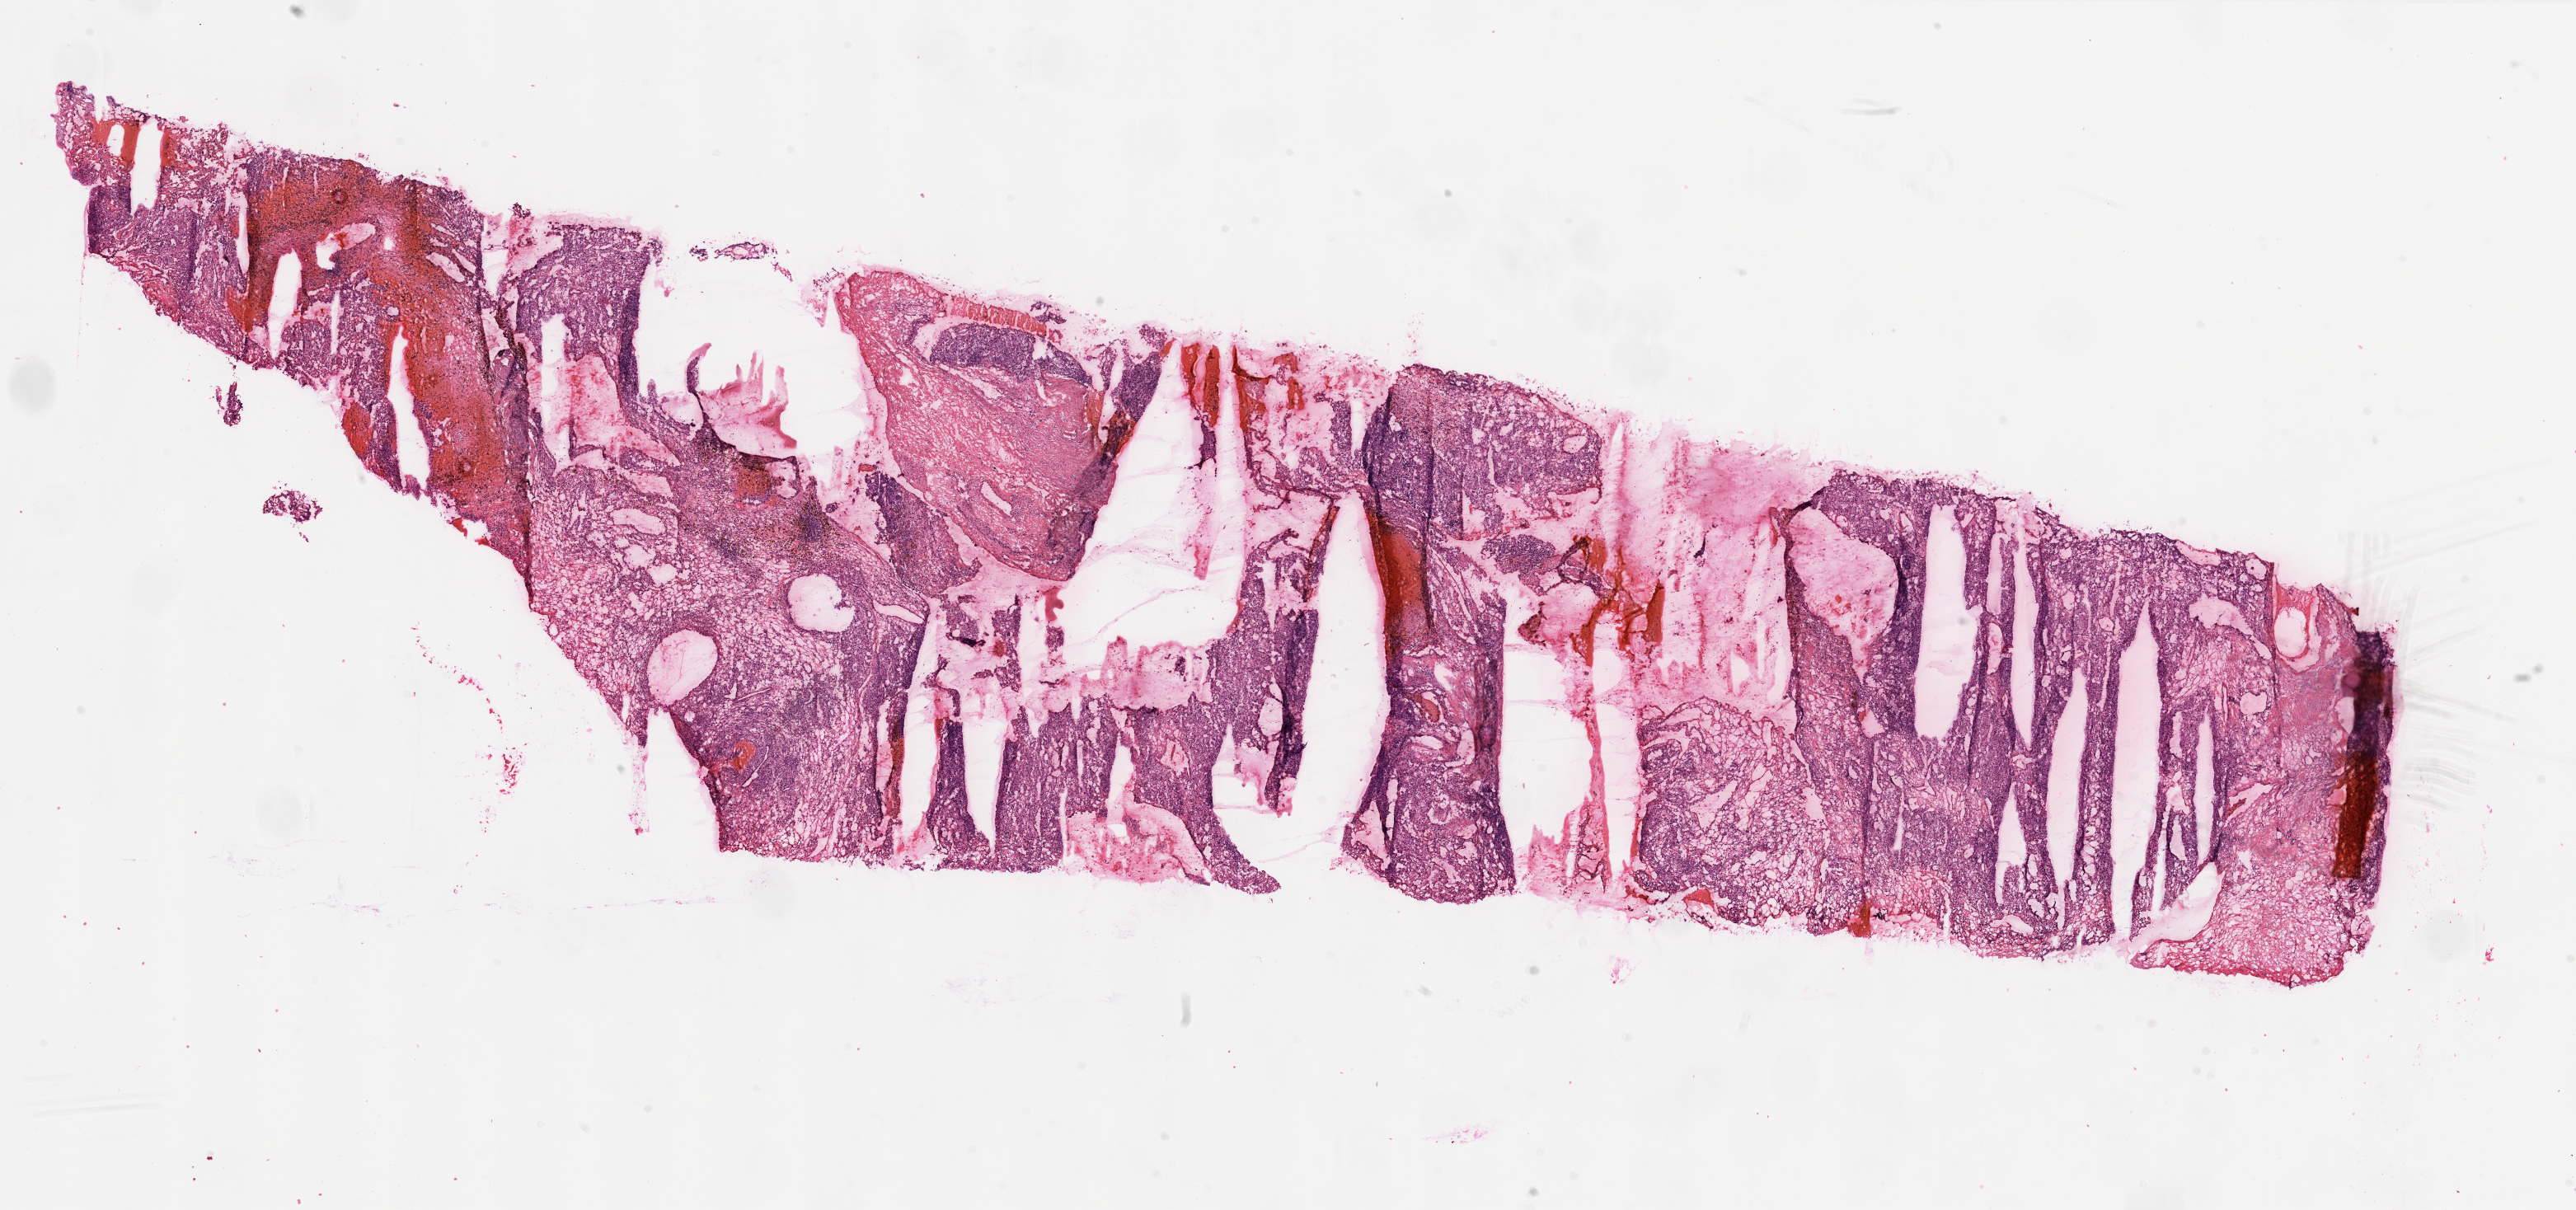
Digitized Hematoxylin and eosin (H&E) stained tissue section (whole slide), low-resolution overview of the scanned area, about 25.1 x 11.8 mm. Frozen section from the top of the tissue portion. Sample: primary tumour, kidney. Patient: male, age at initial diagnosis 64 years. Histologic grade: G4 (undifferentiated). Composition of this section per pathologist review: tumour cells 90%, tumour nuclei 85%, normal cells 0%, stromal cells 10%, necrosis 0%.
Lymph nodes positive (case pathology): 0 of 1 examined. Laterality: left. Histologic diagnosis: Clear cell adenocarcinoma, NOS. AJCC pathologic stage: IV.